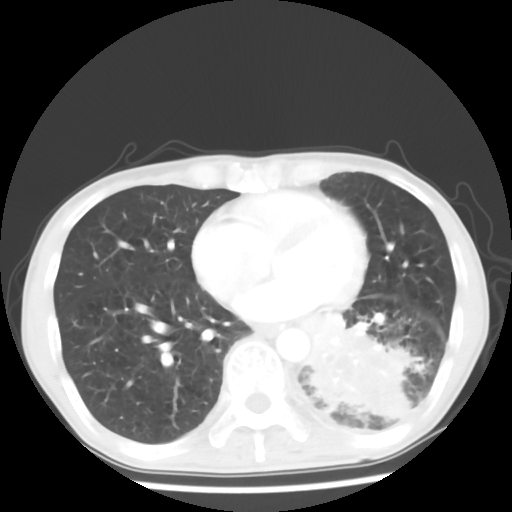
Chest CT, one axial slice; position 24 of 64 along the scan axis; reconstruction kernel STANDARD; 120 kVp; lung window (W 1500 / L -600 HU); 512 × 512 image matrix, field of view 313 × 313 mm. Male patient, age 68 years. Case-level facts recorded for this patient, not image findings: clinical TNM (as recorded): T4 N0 M0.
Annotated regions visible in this slice (bounding box drawn by a radiologist):
- lung tumour (recorded histology: squamous cell carcinoma): bounding box (x1, y1, x2, y2) in pixels: (300, 308, 426, 433)